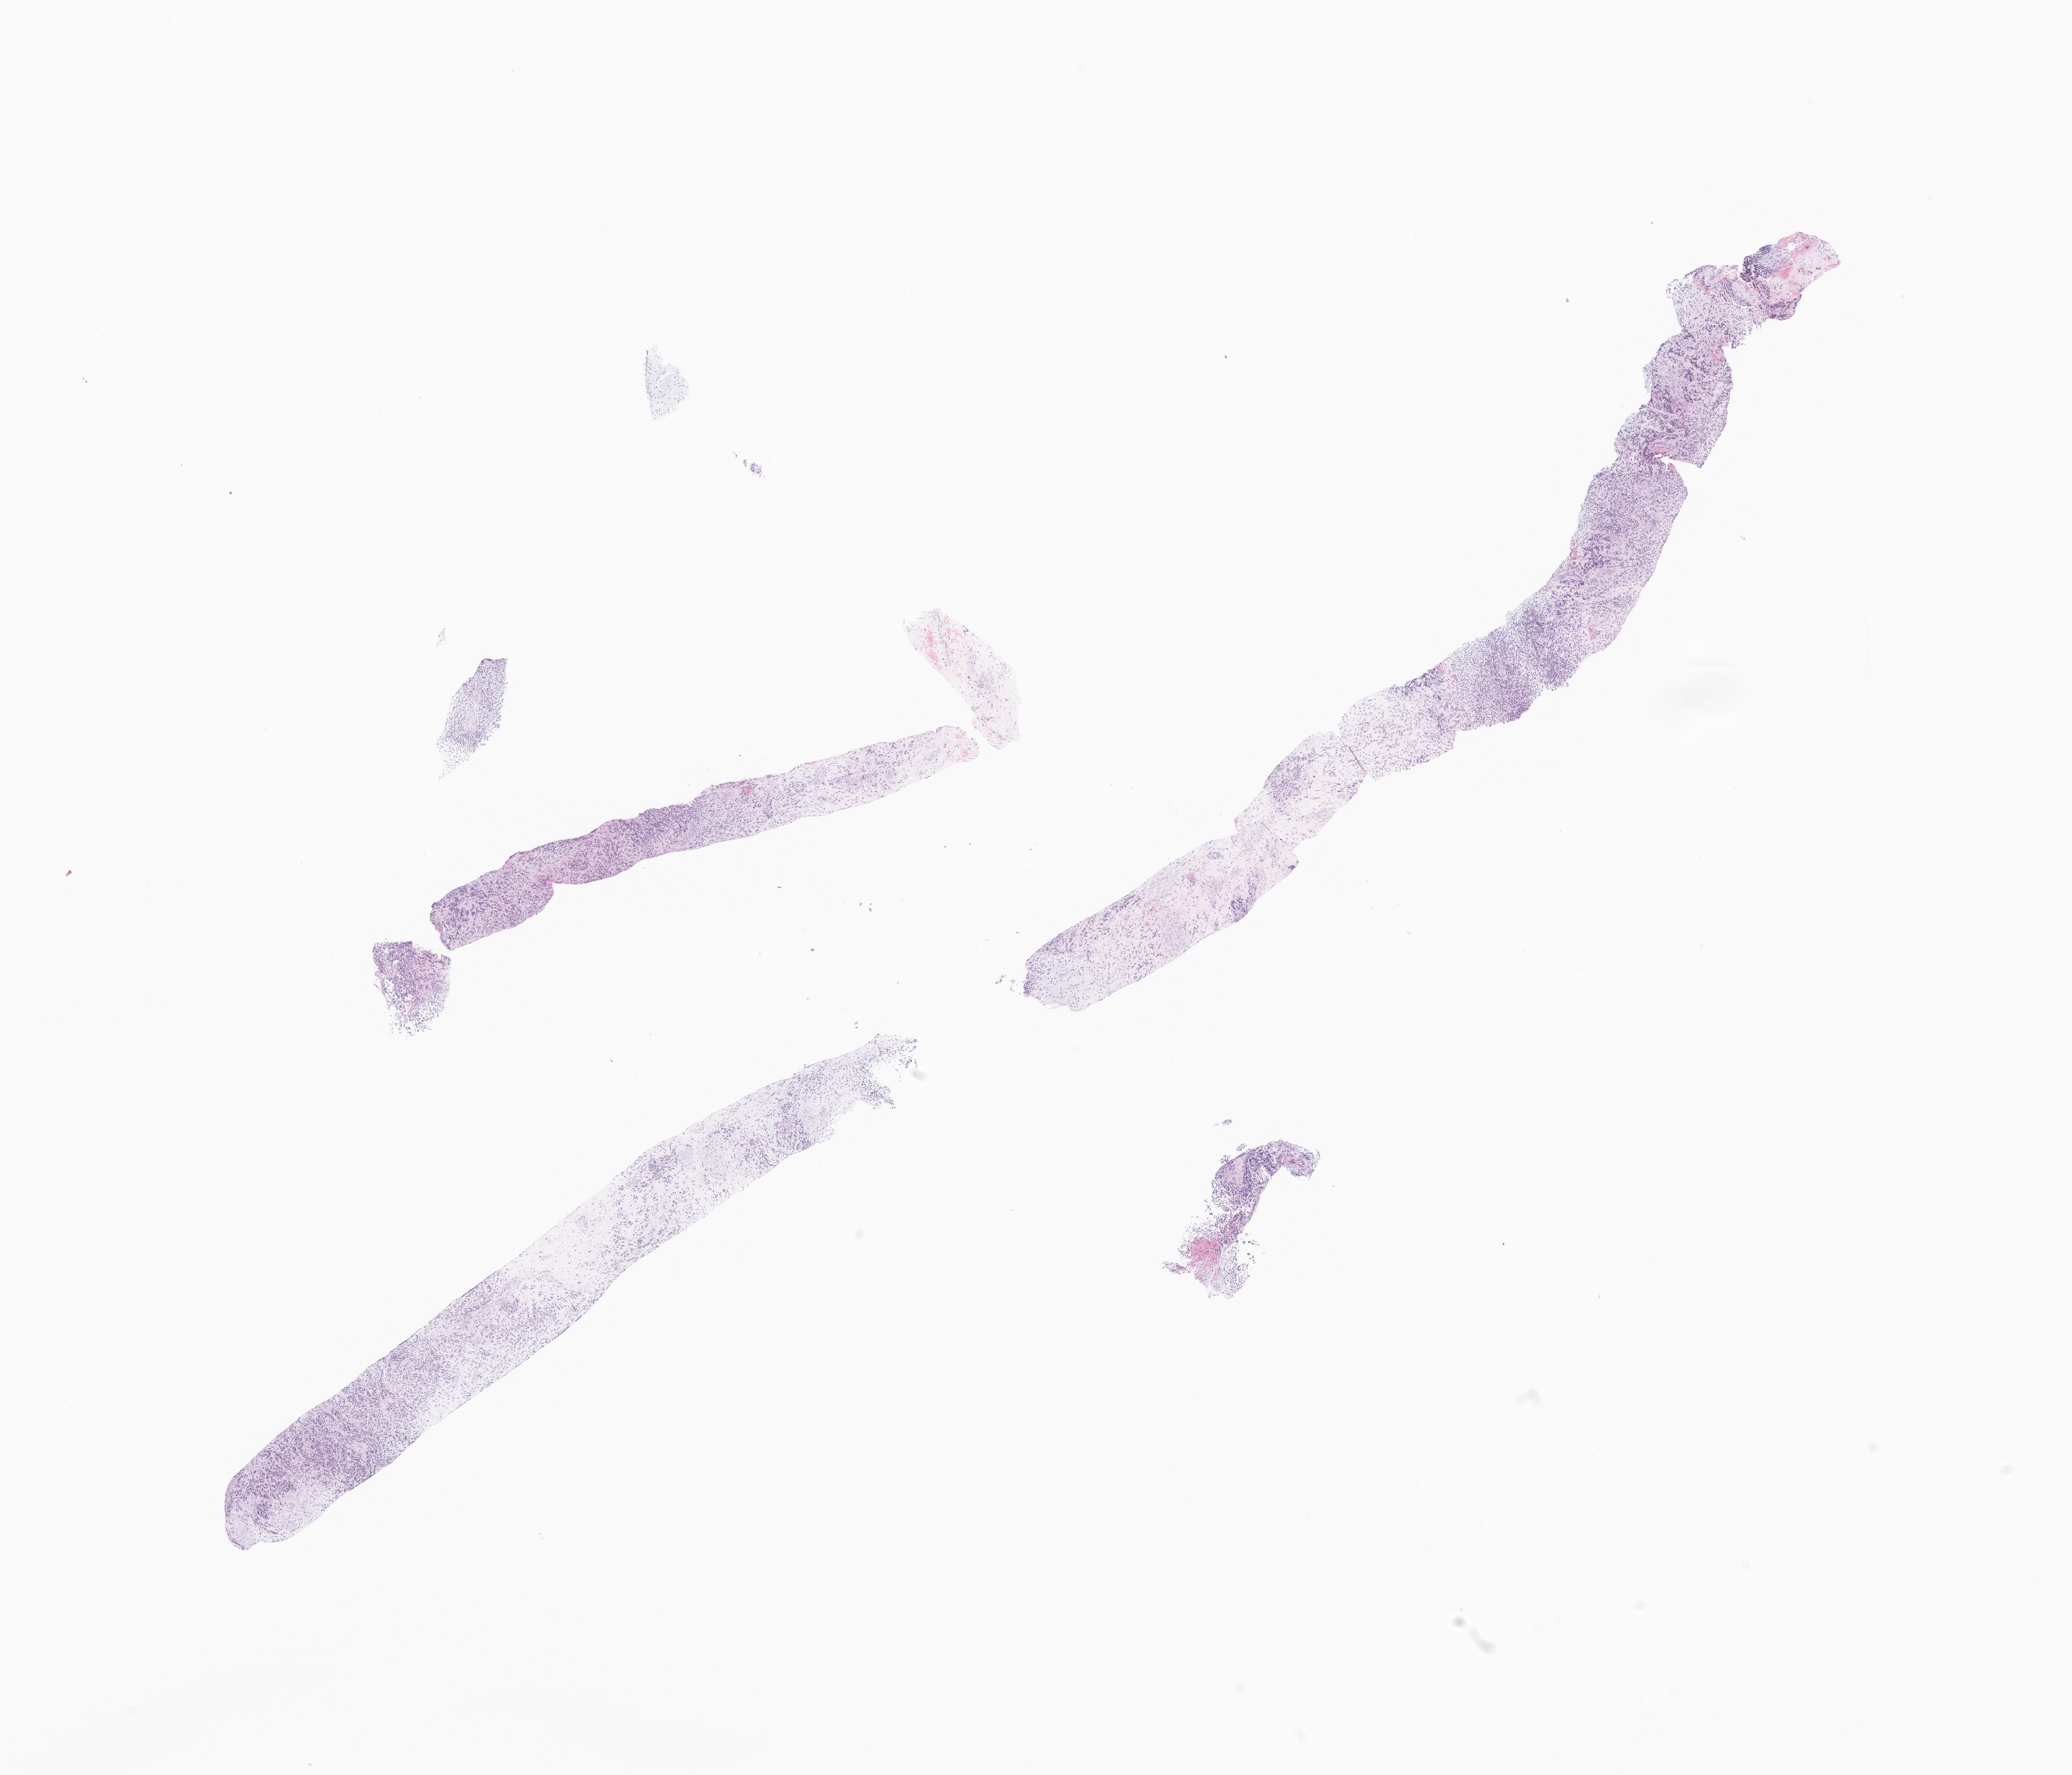
Digitized hematoxylin and eosin (H&E)-stained section of tumor tissue from the soft tissue of pelvis — shown as a low-resolution overview of the whole scanned area (about 17.9 x 15.3 mm), formalin-fixed, paraffin-embedded (FFPE) tissue. Patient male; age 182 months.
- diagnosis (ICD-O-3 morphology term): Rhabdomyosarcoma, NOS
- tissue or organ of origin (case record): connective, subcutaneous and other soft tissues of pelvis